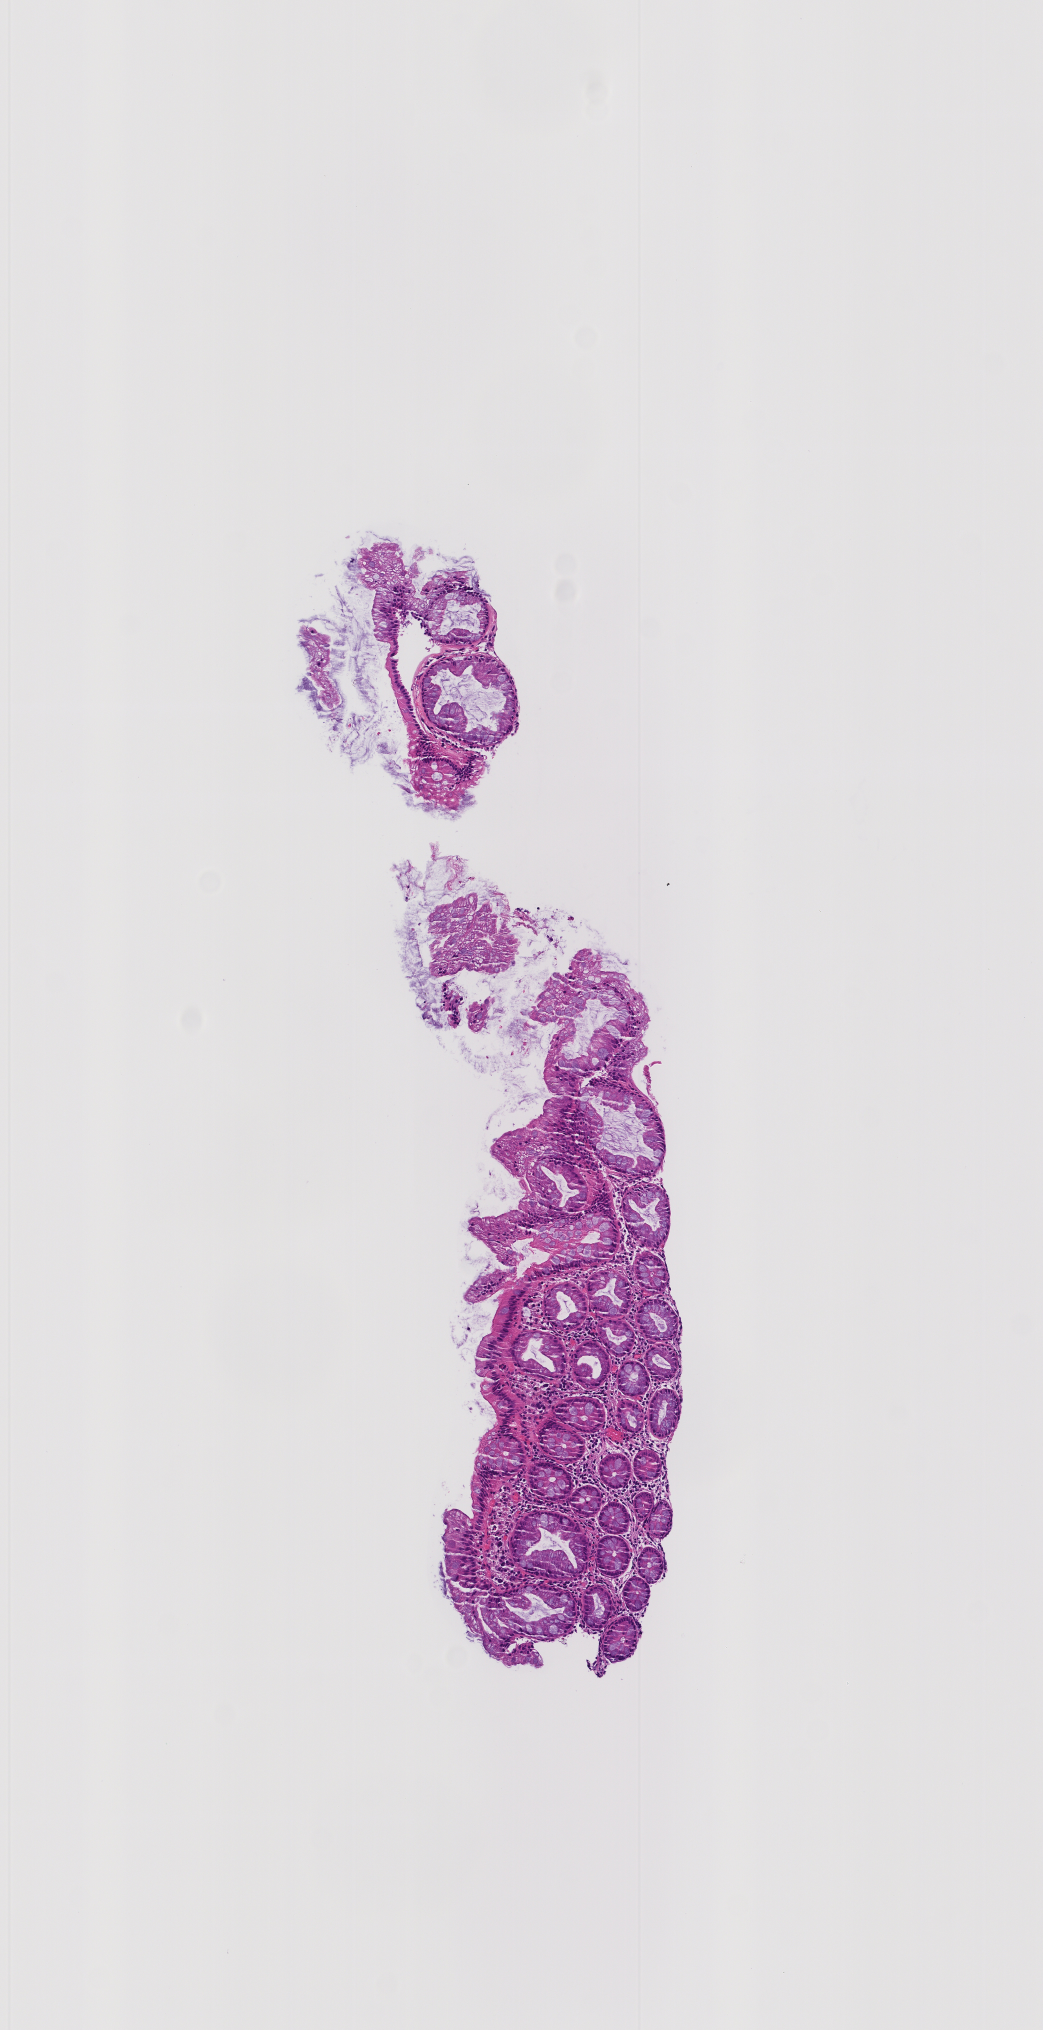
H&E whole-slide image of a colon biopsy, whole scanned area (about 2.1 x 4.1 mm) shown as a low-resolution overview, formalin-fixed paraffin-embedded section, transverse colon. Patient: male.
Lesion category (as recorded): hyperplasia.